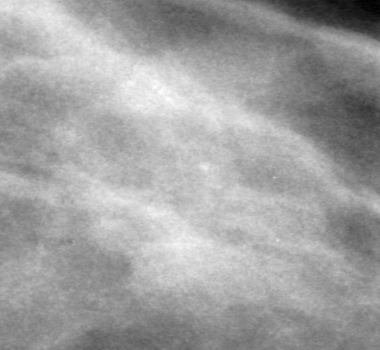
Cropped region of a digitized screen-film mammogram centred on a radiologist-marked abnormality, left breast, CC view, BI-RADS breast density category 2 (scale 1–4).
Finding: mass, shape lobulated, margins obscured; BI-RADS assessment category 0 (incomplete: needs additional imaging); subtlety rating 3 on a 1 (subtle) to 5 (obvious) scale; pathology (as recorded): benign.